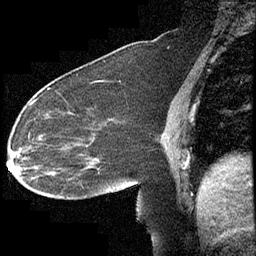
Breast MRI (dynamic contrast-enhanced), one sagittal slice. Position 158 of 232 along the scan axis. Dynamic contrast-enhanced study with each time point stored as its own series, time point 2 of 4 at this slice position (early post-contrast, ordered by acquisition time). 1.5 T. TE 4.2 ms, TR 6.7 ms. 3 mm slice thickness. 256 × 256 image matrix, field of view 200 × 200 mm. Patient: female, 63 years. From the clinical record (not read from this slice): setting: breast cancer imaged before/during neoadjuvant chemotherapy; receptor status: triple-negative.
Structures marked on this image (semi-automatic segmentation, software-assisted and operator-edited):
- analysis volume of interest (the breast-tissue region the enhancement analysis was run in; not a lesion): bounding box [x1, y1, x2, y2] px = [13, 90, 140, 211]
- tumour enhancement mask (voxels above the 70 % enhancement threshold inside the analysis volume of interest): [13, 99, 36, 158]